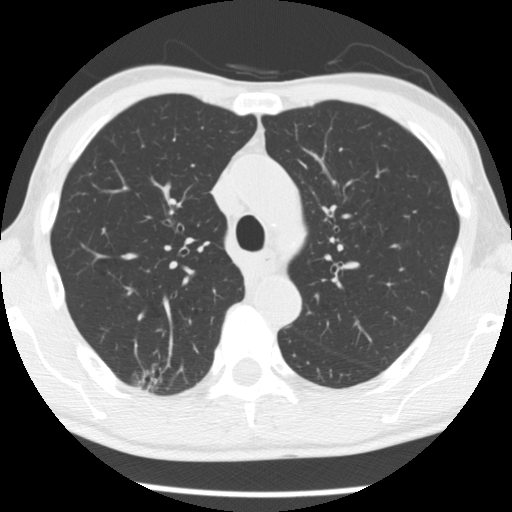
Chest CT (low-dose screening protocol), one axial image; baseline annual screen; lung window (W 1500 / L -600 HU); 2.5 mm slice thickness; slice 84 of 277 in the series. Male participant, aged 66 years at enrolment.
Expert-annotated lung lesion, box from (x=132, y=356) to (x=190, y=401) px. The screening reader recorded 4 non-calcified nodules or masses ≥4 mm on this exam (right upper lobe, right upper lobe, right upper lobe, left lower lobe); which of them this box marks is not recorded. Official screen result: positive, change unspecified: nodule(s) >= 4 mm or enlarging nodule(s), mass(es), or other non-specific abnormalities suspicious for lung cancer. Later outcome: lung cancer diagnosed 503 days after this screen — adenocarcinoma, NOS, right upper lobe, undifferentiated (G4), stage IA (AJCC 6th edition), 20 mm at pathology.